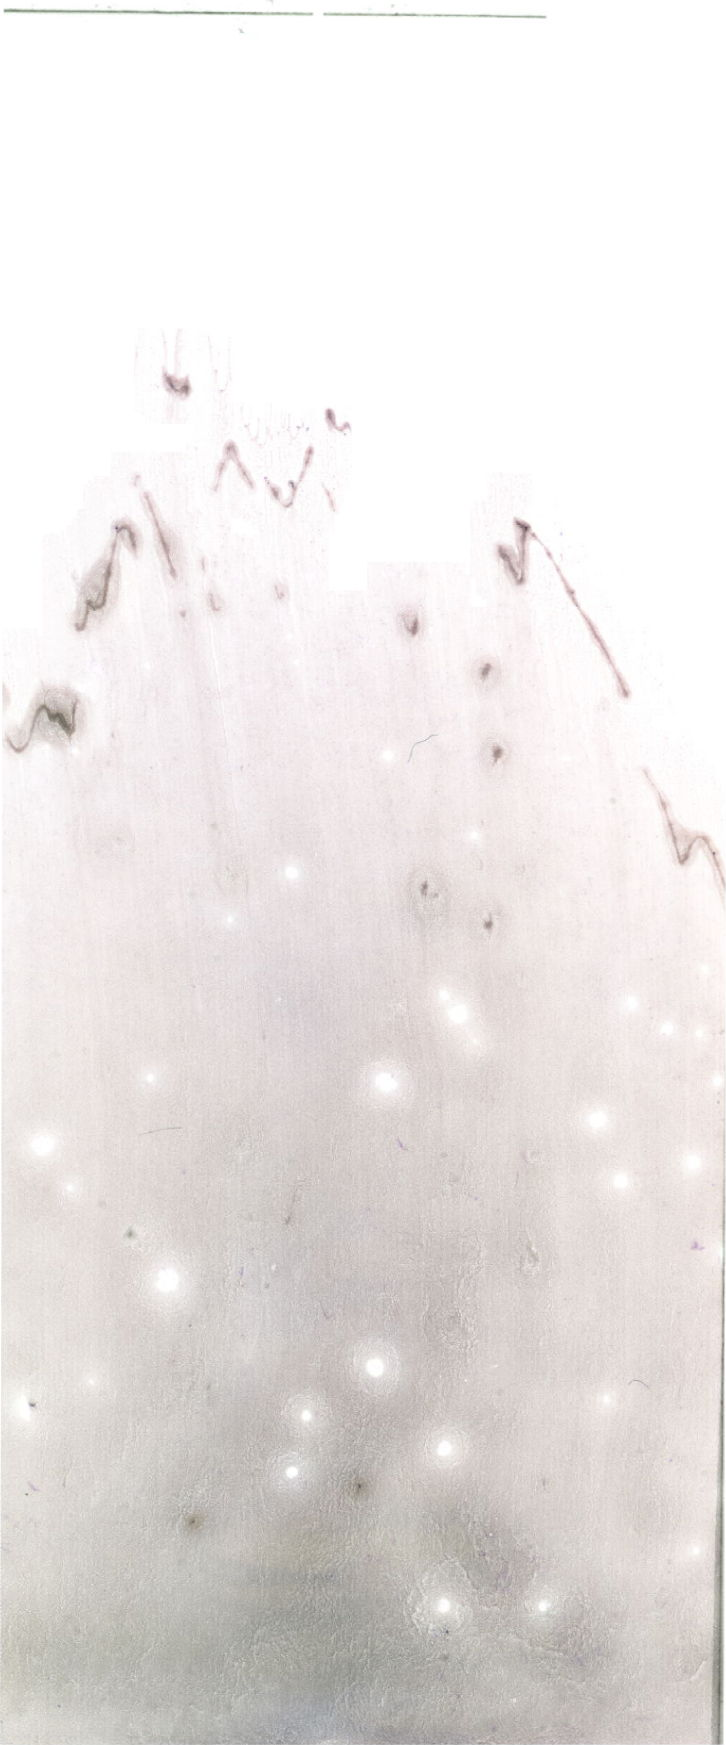
Bone marrow aspirate smear, May-Grünwald–Giemsa stain, whole-slide image — a low-resolution overview of the entire scanned area, about 20.6 x 49.5 mm. Patient sex: male.